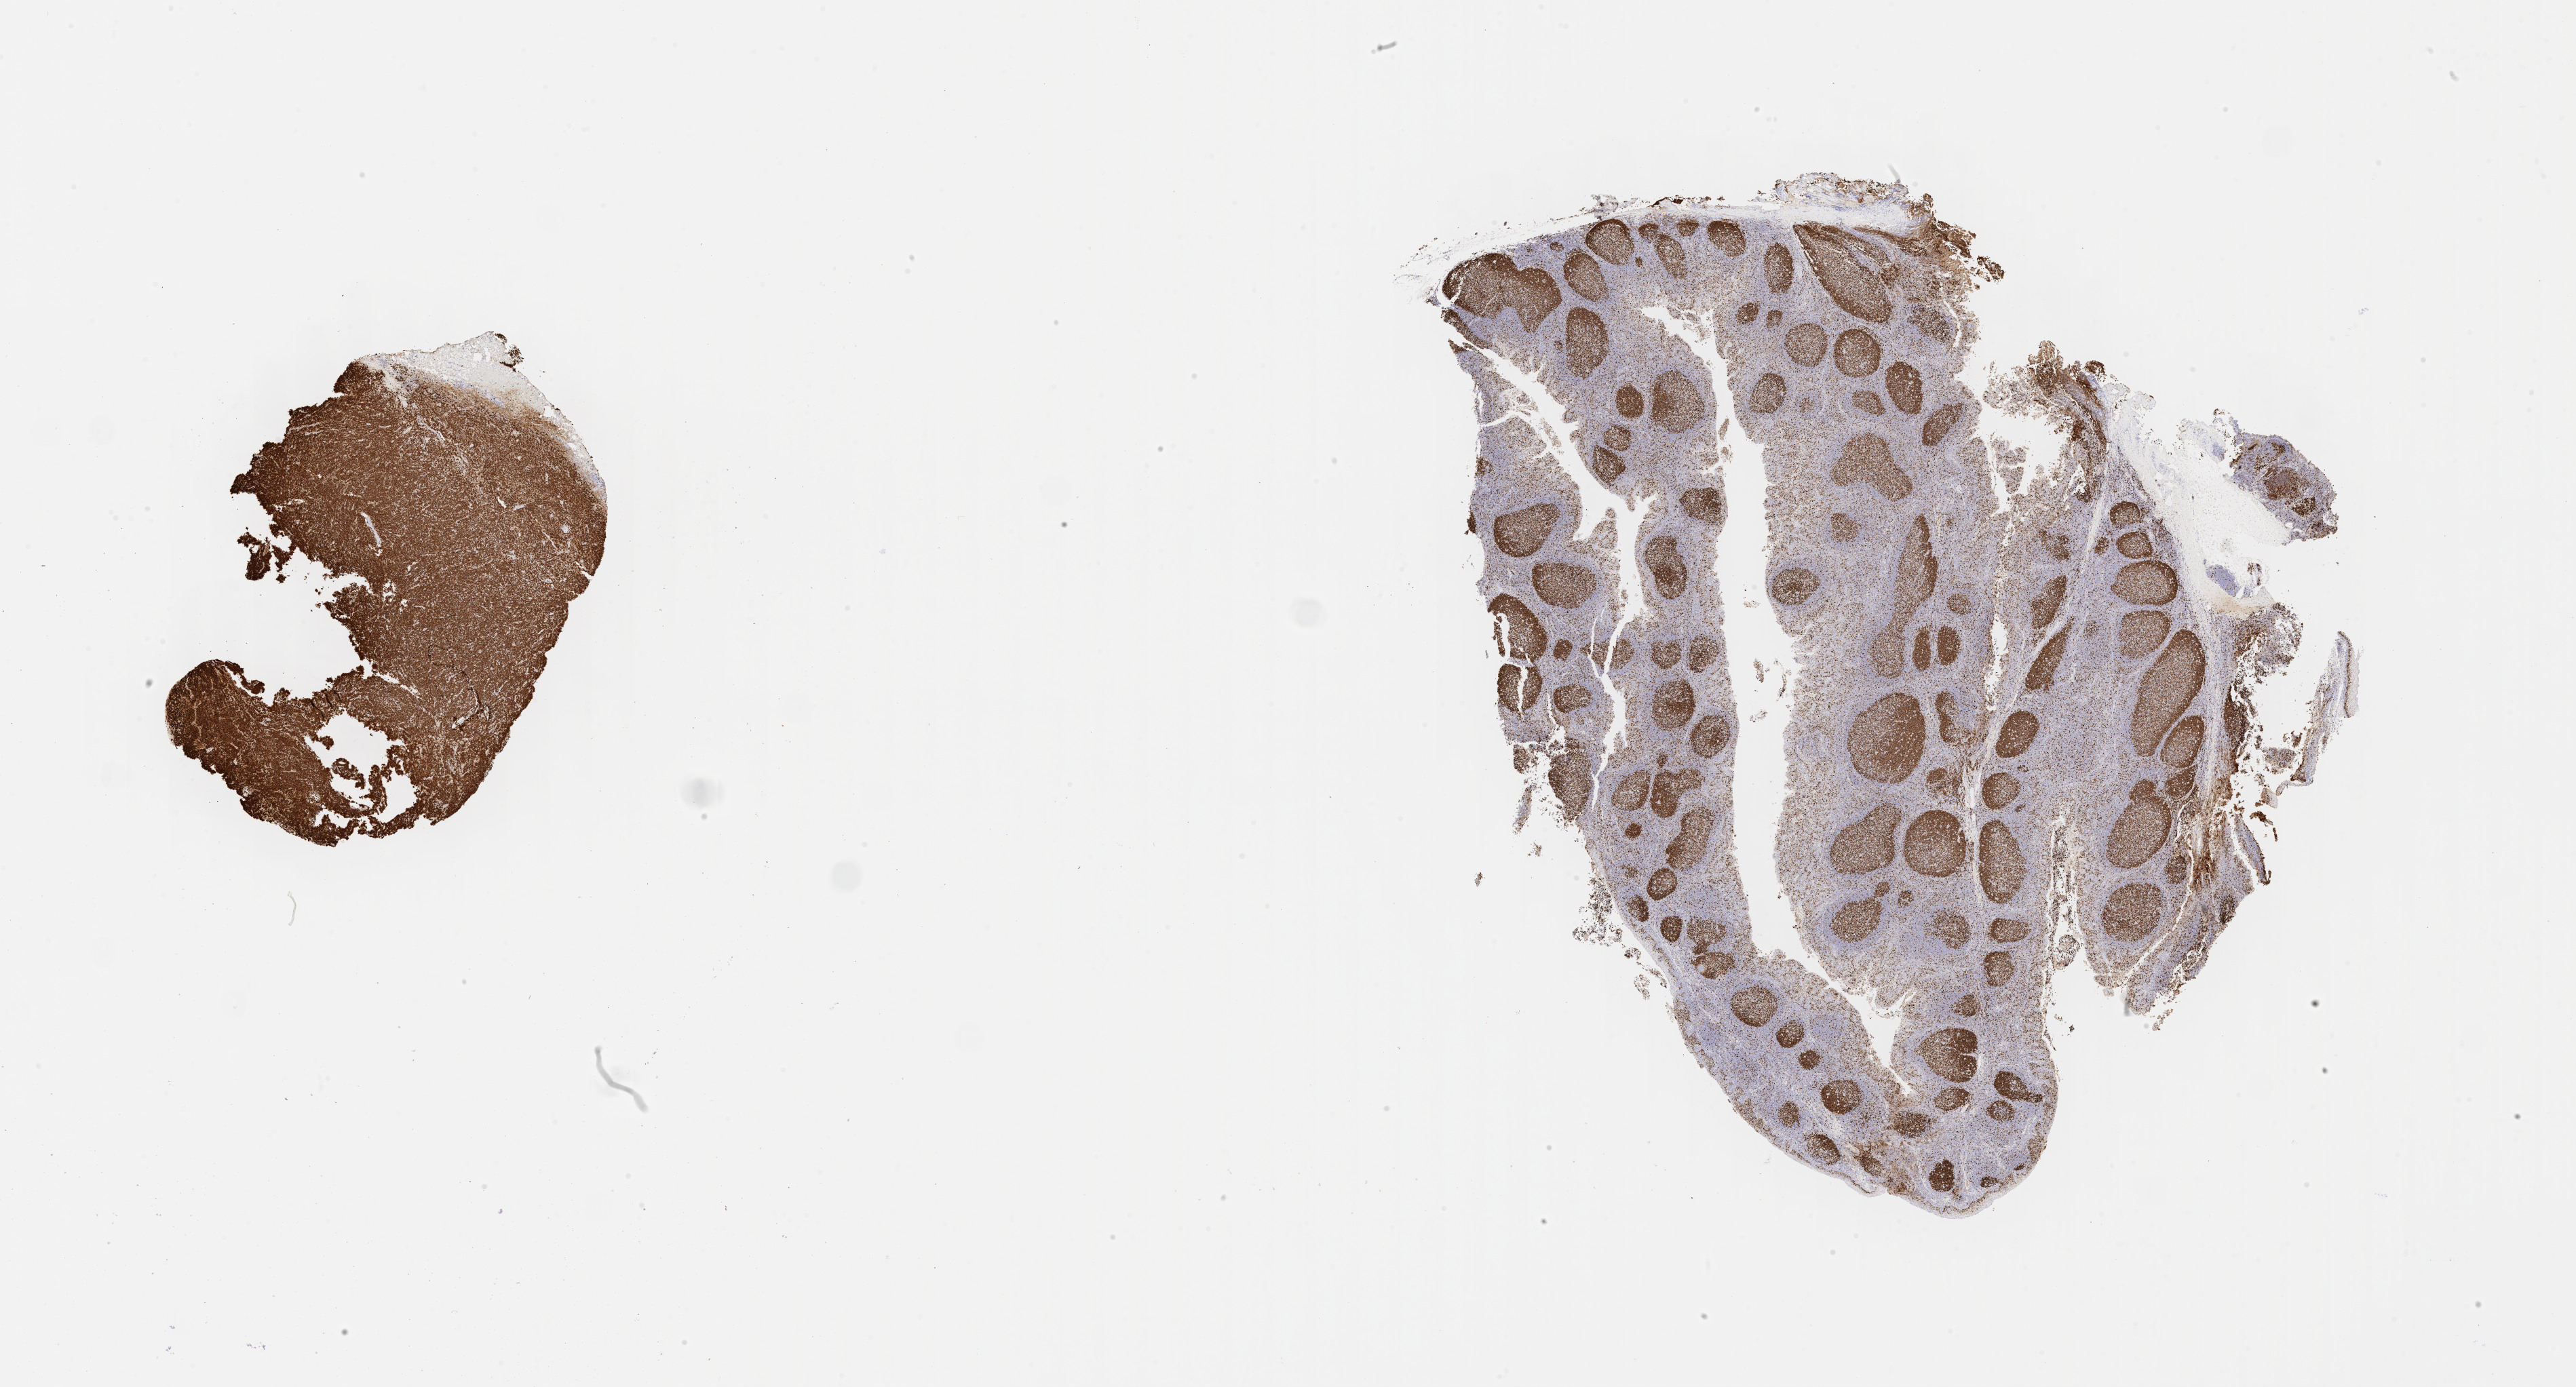
Whole-slide image, immunohistochemical stain for Ki-67 — low-resolution overview of the scanned area, about 30.7 x 16.5 mm. Specimen: tumor tissue. Site: mandible. Patient: female, age at initial diagnosis 7 years.
Histologic diagnosis: Burkitt lymphoma, NOS.